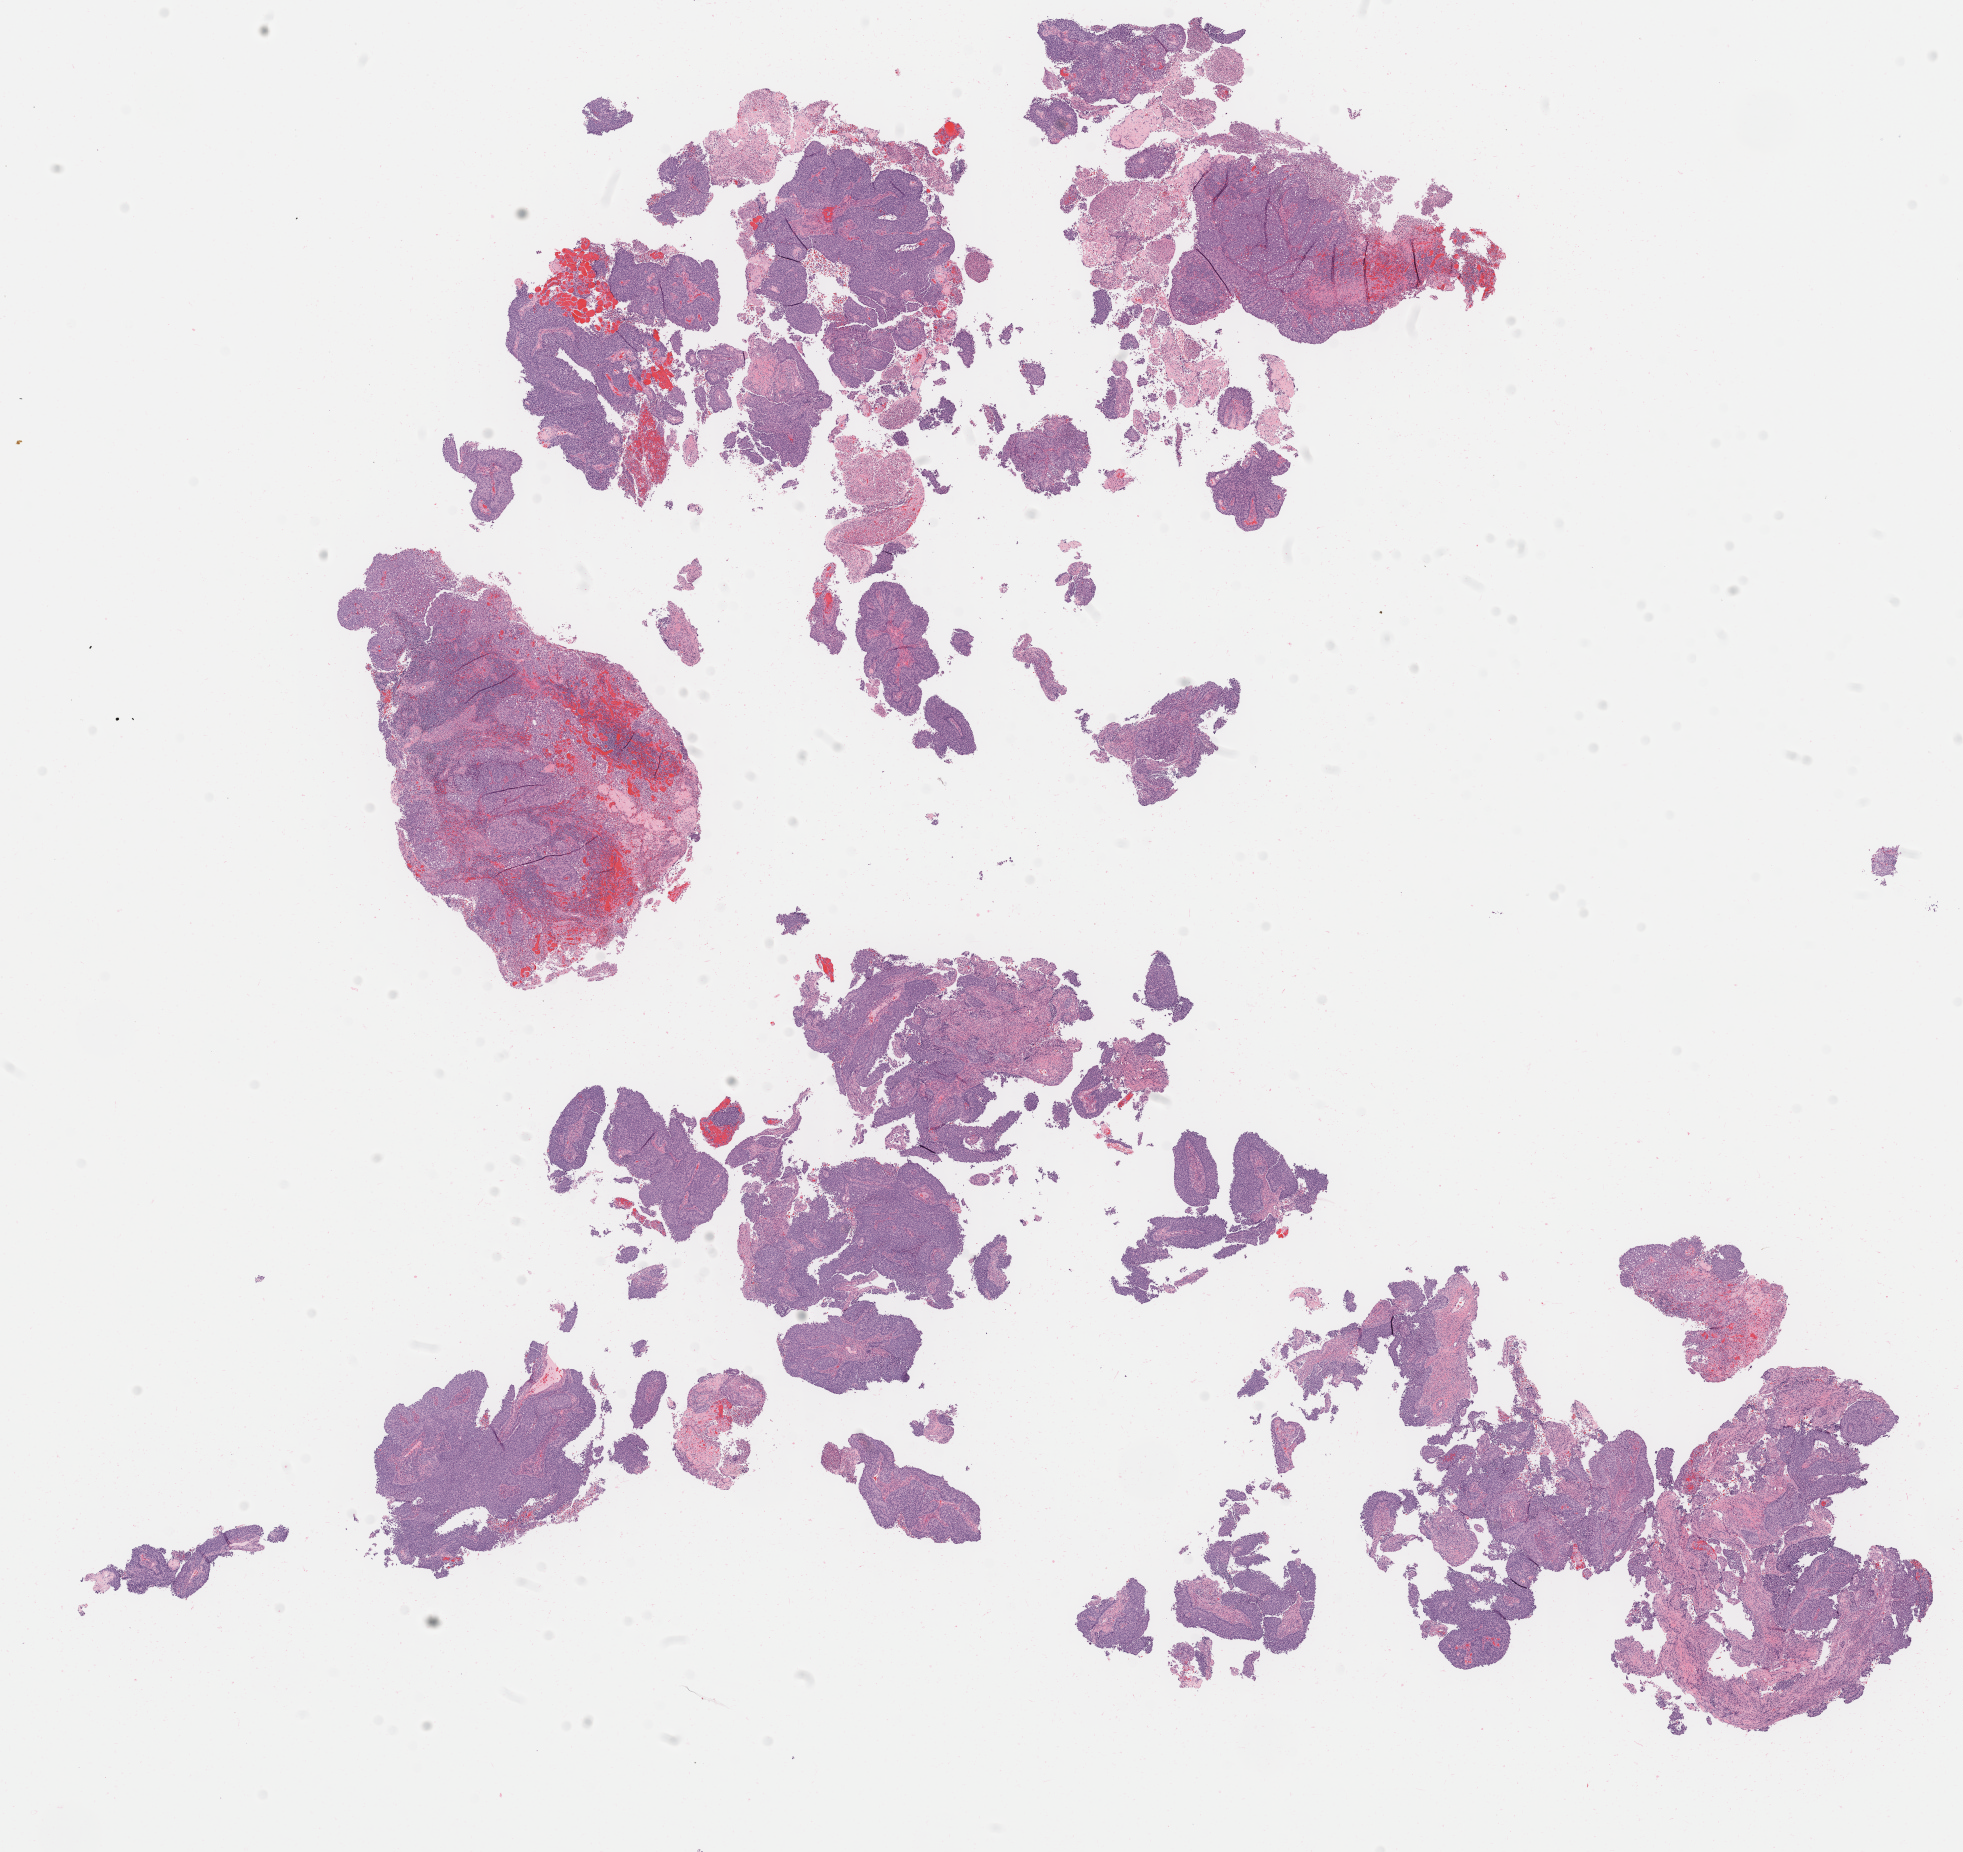
Hematoxylin and eosin (H&E) whole-slide image — low-resolution overview of the scanned area, about 15.6 x 14.7 mm. Tumor tissue. Site: cervix. Patient: female, 40 years old.
Histologic diagnosis: Adenocarcinoma, NOS.